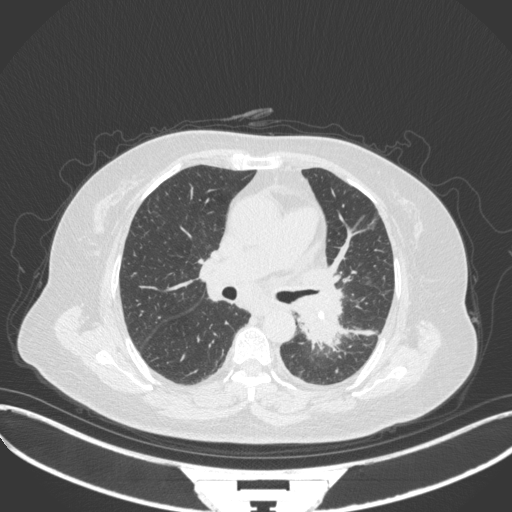
Chest CT, one axial slice. Position 202 of 328 along the scan axis. Lung window (W 1500 / L -600 HU). 512 × 512 image matrix, field of view 400 × 400 mm. Female patient, age 69 years. Case-level facts recorded for this patient, not image findings: clinical TNM (as recorded): T2b N3 M1.
Structures marked on this image (bounding box drawn by a radiologist):
- lung tumour (recorded histology: adenocarcinoma): bounding box (x1, y1, x2, y2) in pixels: (290, 290, 350, 353)